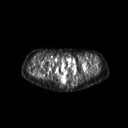
FDG PET of an extremity soft-tissue mass (from a PET/CT study), one axial slice; position 56 of 267 along the scan axis; 3.27 mm slice thickness; 128 × 128 image matrix, field of view 600 × 600 mm. Female patient, age 57 years. From the clinical record (not read from this slice): histological type: epithelioid sarcoma with vascular differentiation; site of the primary tumour: right buttock.
Structures marked on this image (expert contour drawn on MRI and transferred to this co-registered scan by the dataset authors):
- gross tumour volume (mass): bounding box <28,67,38,74> (left, top, right, bottom; pixels)